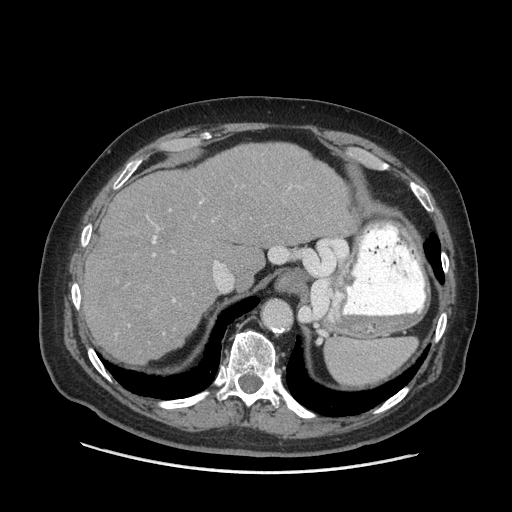
Contrast-enhanced abdominal CT (liver protocol), one axial slice; slice 52 of 77 in the series (ordered by position); reconstruction kernel STANDARD; 140 kVp; soft-tissue window (W 400 / L 40 HU); 2.5 mm slice thickness; 512 × 512 image matrix, field of view 420 × 420 mm. Case-level facts recorded for this patient, not image findings: diagnosis: hepatocellular carcinoma (patient treated with transarterial chemoembolisation; whether this scan precedes or follows treatment is not stated here); TNM stage (as recorded): Stage-I; Child-Pugh class: A.
Outlined on this slice (semi-automatic segmentation, software-assisted and operator-edited):
- liver parenchyma outside the tumour (the mass and vessels are separate outlines, so this box may not span the whole liver): bounding box [x1, y1, x2, y2] px = [84, 142, 356, 364]
- liver vessels: [152, 202, 218, 302]